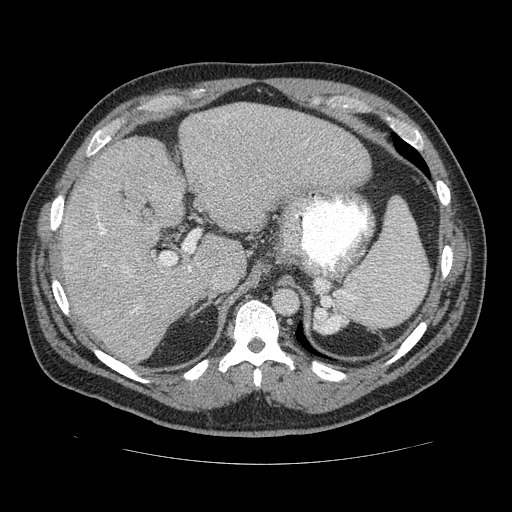
Contrast-enhanced abdominal CT (liver protocol), one axial slice. Position 89 of 113 along the scan axis. Reconstruction kernel STANDARD. 120 kVp. Soft-tissue window (W 400 / L 40 HU). 2.5 mm slice thickness. 512 × 512 image matrix. Case-level facts recorded for this patient, not image findings: diagnosis: hepatocellular carcinoma (patient treated with transarterial chemoembolisation; whether this scan precedes or follows treatment is not stated here); TNM stage (as recorded): Stage-II; Child-Pugh class: B; tumour differentiation: moderately differentiated; tumour size: 4.8 cm.
Annotated regions visible in this slice (semi-automatic segmentation, software-assisted and operator-edited):
- liver parenchyma outside the tumour (the mass and vessels are separate outlines, so this box may not span the whole liver): box from (x=52, y=104) to (x=374, y=362) px
- mass: (x=150, y=266)–(x=170, y=293)
- liver vessels: (x=64, y=177)–(x=215, y=314)